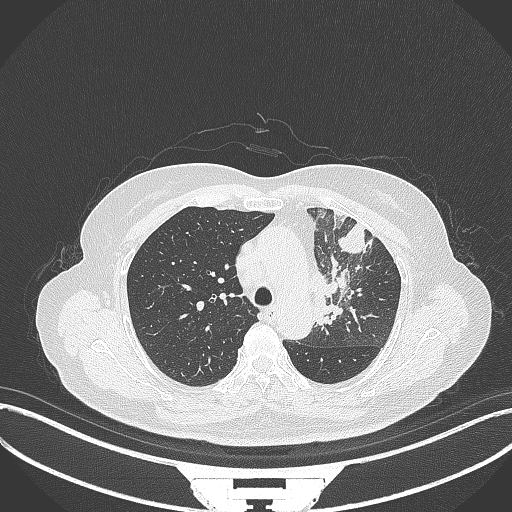
Chest CT, one axial slice; reconstruction kernel B70f; lung window (W 1500 / L -600 HU); 512 × 512 image matrix, field of view 400 × 400 mm. Female patient, age 64 years. From the clinical record (not read from this slice): clinical TNM (as recorded): T2a N2 M0.
Annotated regions visible in this slice (rectangle marked by the reading radiologist):
- lung tumour (recorded histology: adenocarcinoma): box from (x=311, y=260) to (x=353, y=328) px
- lung tumour (recorded histology: adenocarcinoma): (x=337, y=220)–(x=369, y=257)